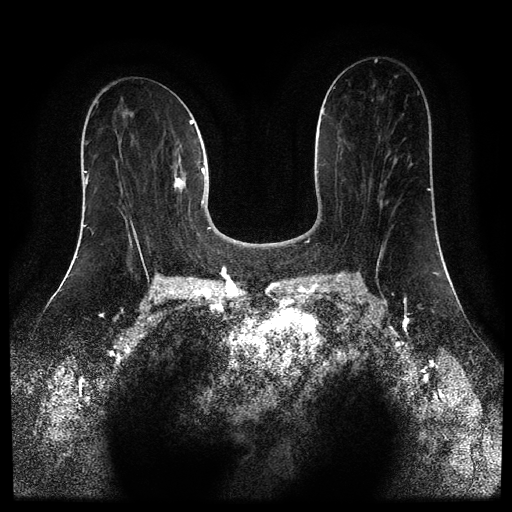
Breast MRI (dynamic contrast-enhanced, multi-phase), one axial slice; position 44 of 110 along the scan axis; dynamic contrast-enhanced series, time point 2 of 5 at this slice position (early post-contrast); 1.5 T; TE 2.6 ms, TR 5.4 ms; 512 × 512 image matrix. Patient: female, 43 years.
Annotated regions visible in this slice (semi-automatically segmented with operator editing):
- breast lesion (labelled 'tumour' in the annotation; benign lesions carry a separate 'benign' label): bounding box <173,174,186,192> (left, top, right, bottom; pixels)